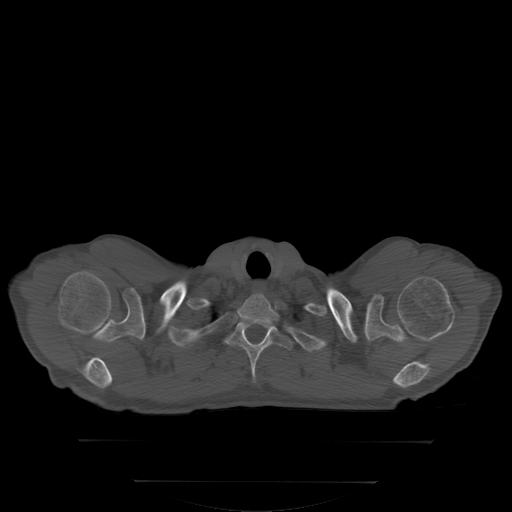
CT including the spine, one axial slice; position 290 of 350 along the scan axis; bone window (W 1800 / L 400 HU); 2.5 mm slice thickness; 512 × 512 image matrix, field of view 500 × 500 mm. Male patient, age 58 years. From the clinical record (not read from this slice): primary cancer: prostate; vertebrae with lytic lesions (as recorded): L1.
Outlined on this slice (semi-automatically segmented with operator editing):
- T1 vertebra: box from (x=203, y=319) to (x=293, y=382) px